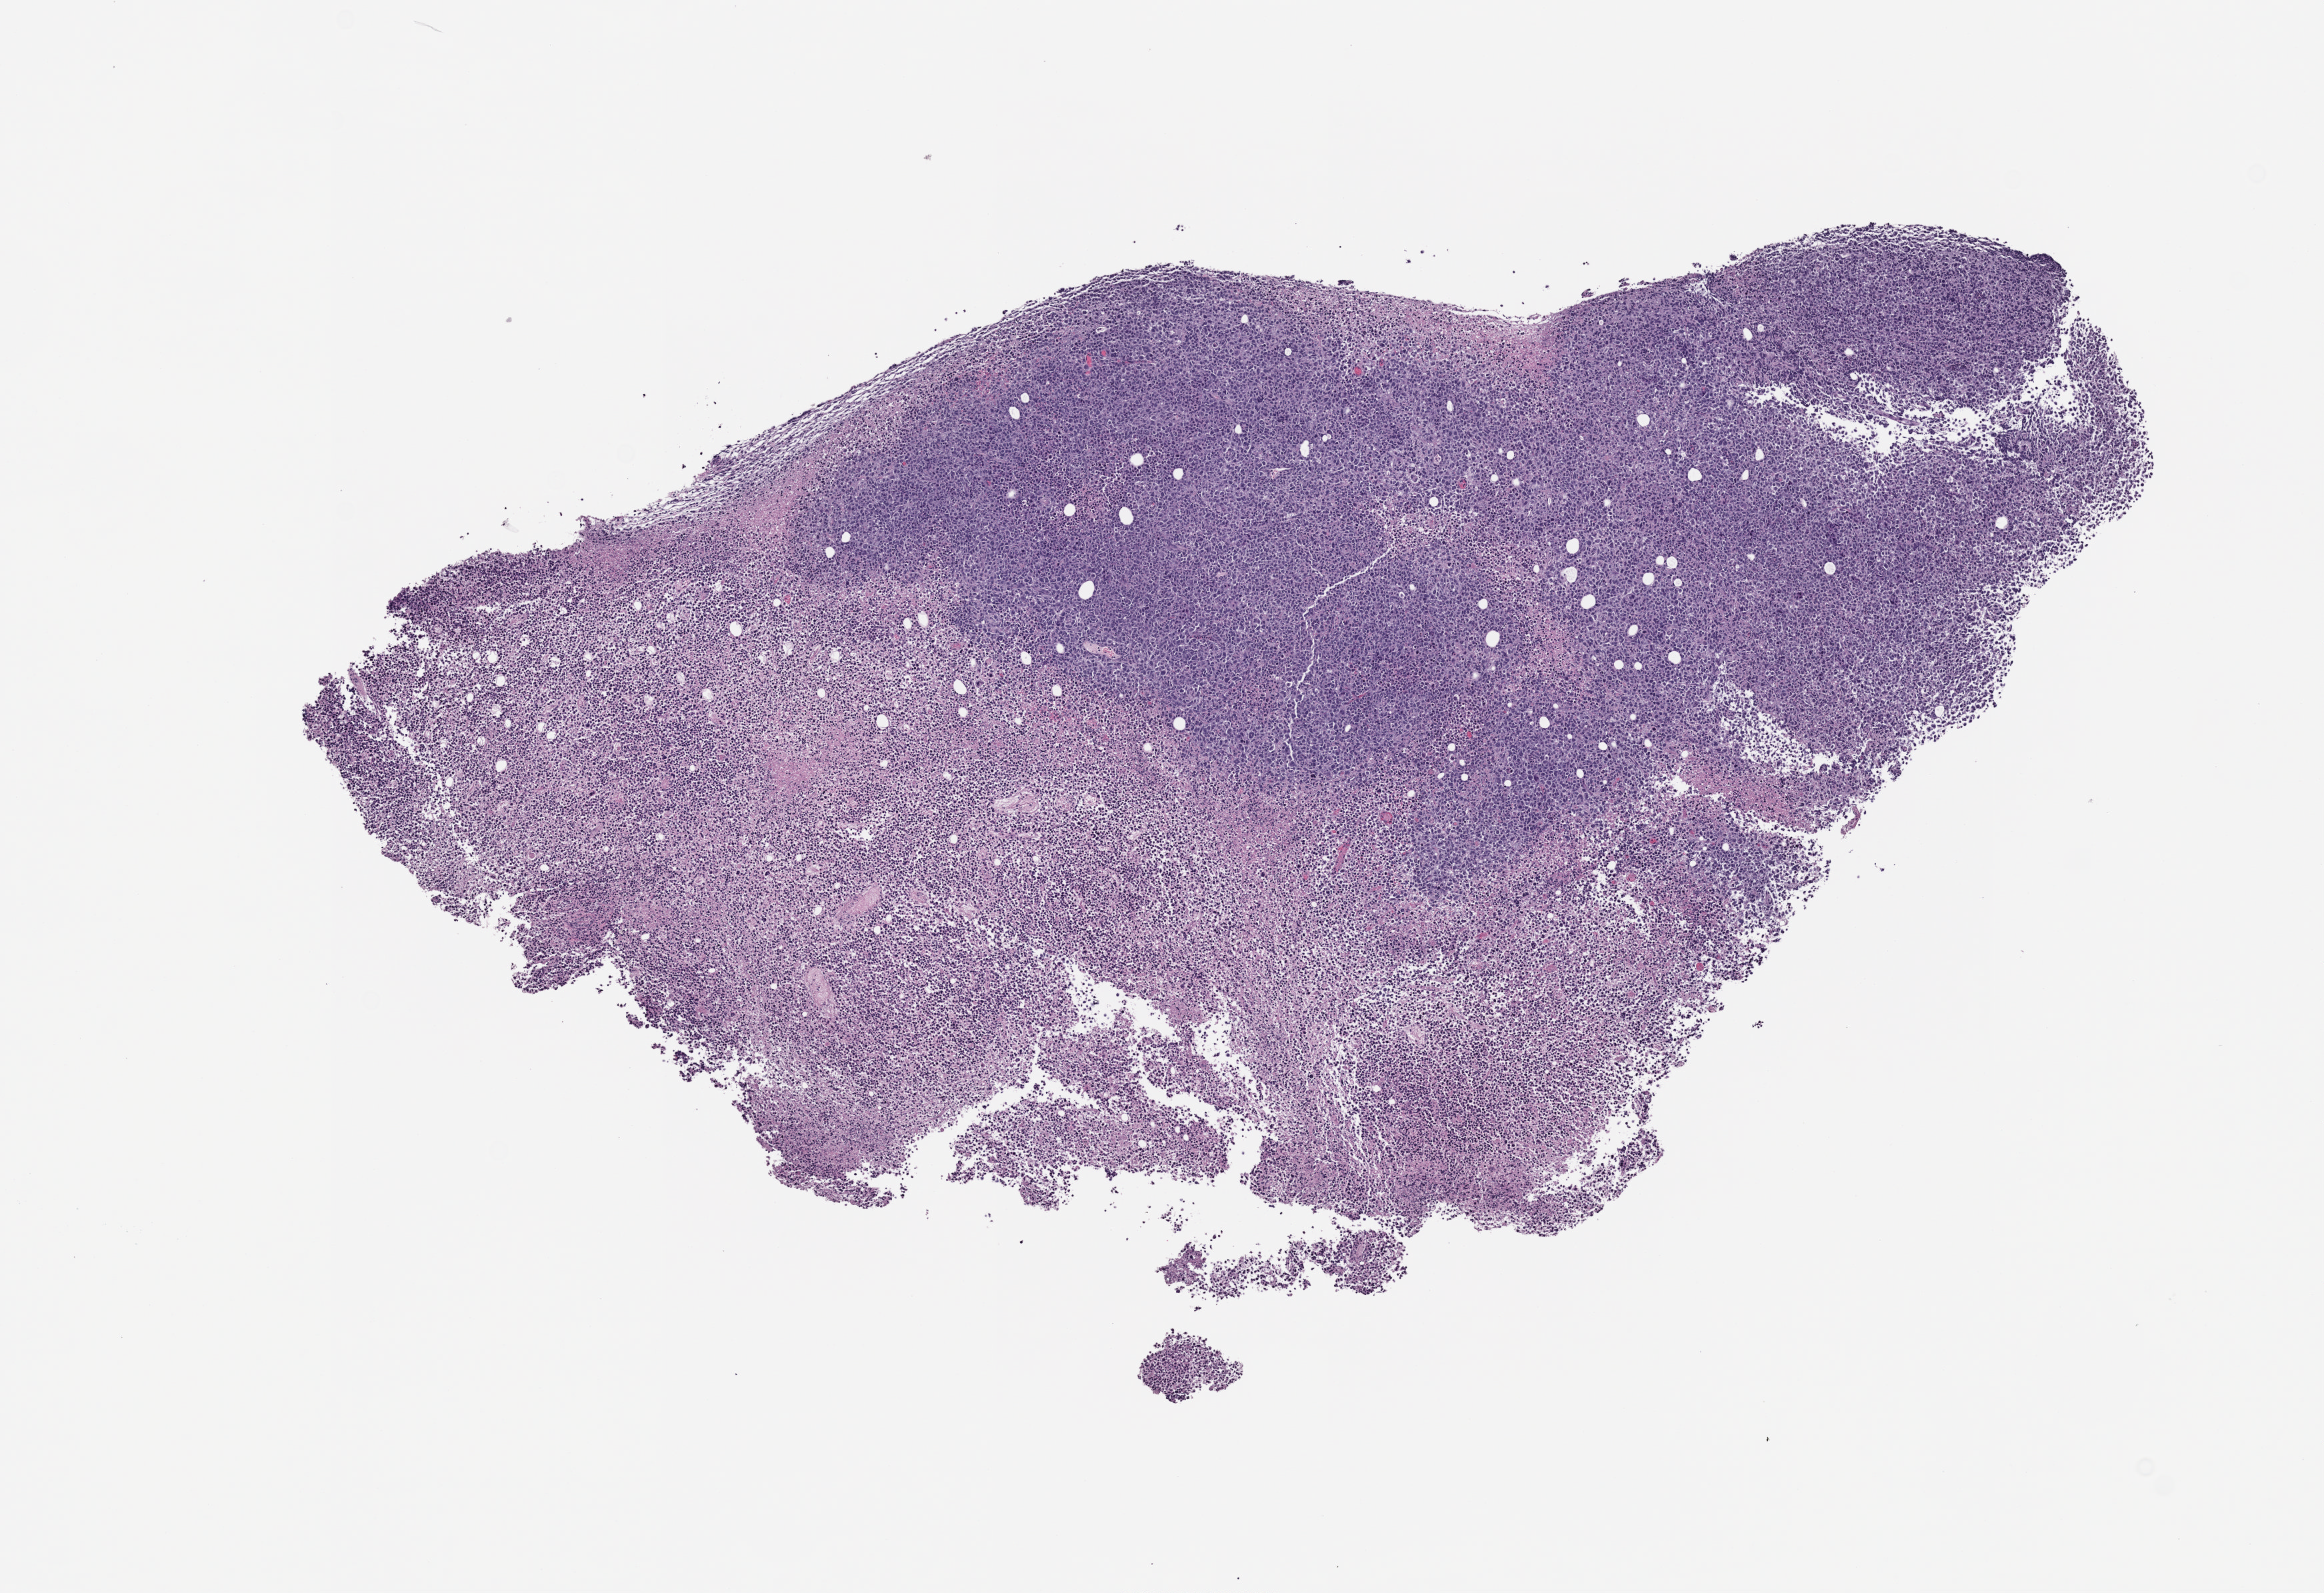
Whole-slide image, hematoxylin and eosin (H&E): patient-derived xenograft (human tumor grown in a mouse), shown as a low-resolution overview of the whole scanned area (about 7.0 x 4.8 mm).
• specimen: formalin-fixed, paraffin-embedded (FFPE) tissue